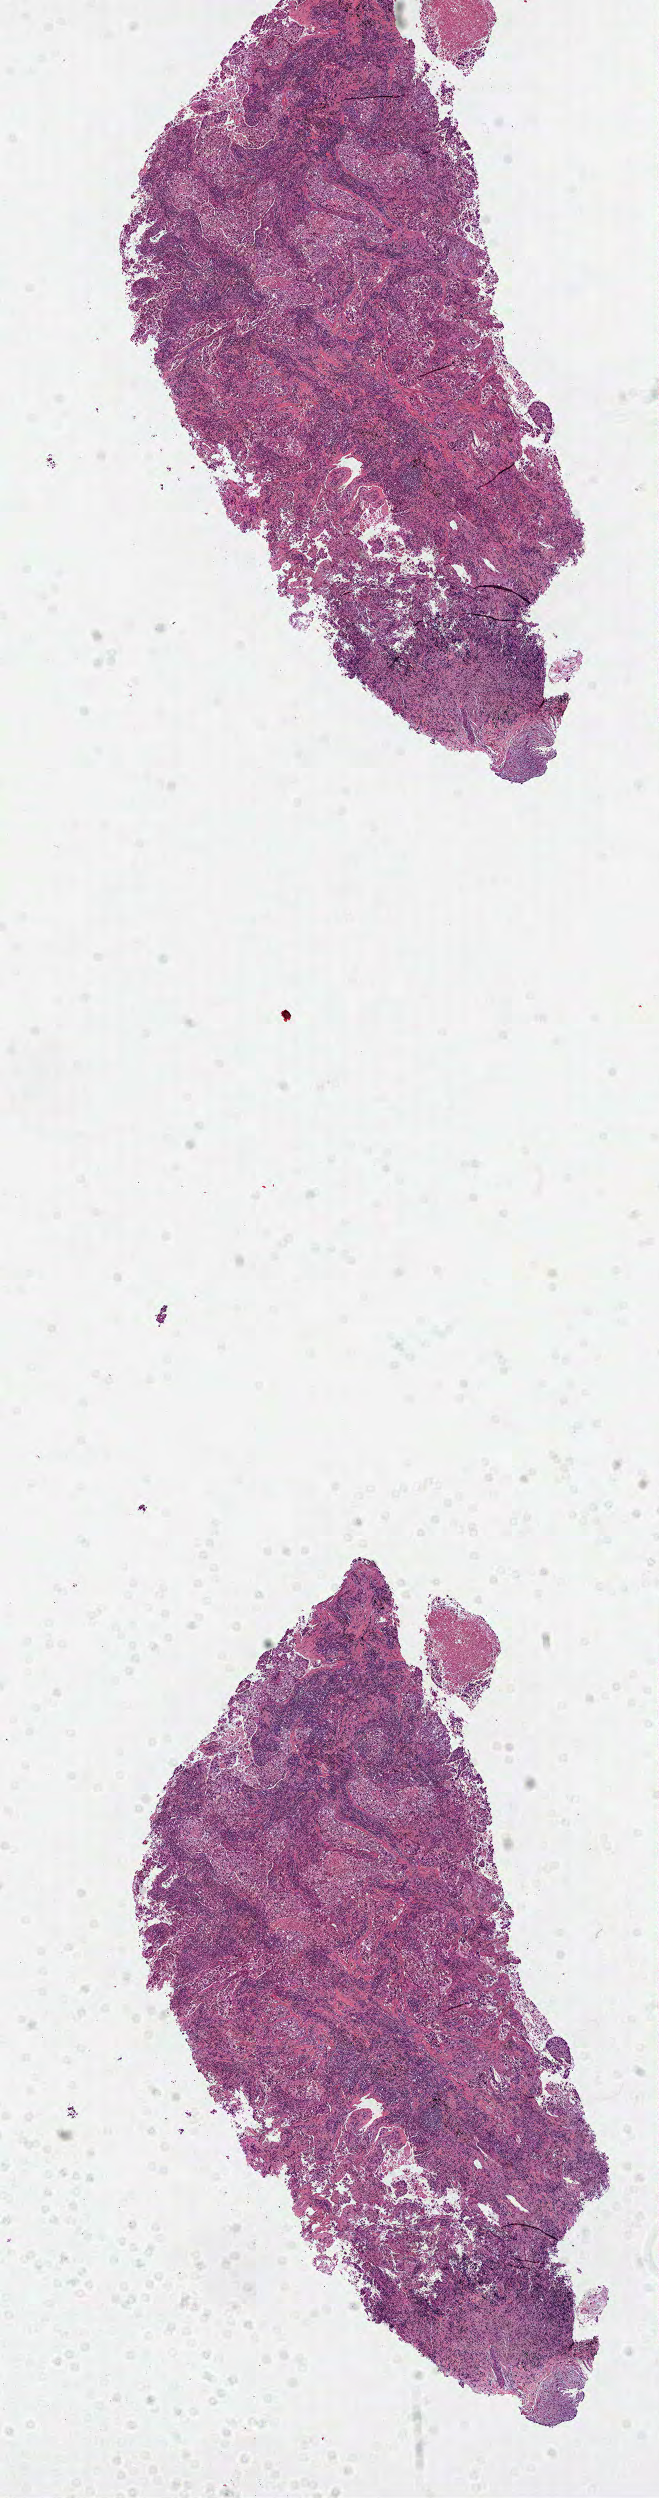
H&E whole-slide image, a low-resolution overview of the entire scanned area, about 5.3 x 20.2 mm (acquisition: 40x scan); formalin-fixed paraffin-embedded (FFPE) diagnostic section; lung, primary tumour sample. Patient: female, age at initial diagnosis 62 years.
* pathologic diagnosis: Squamous cell carcinoma, NOS (upper lobe, lung)
* AJCC pathologic stage: IIIA (6th edition)